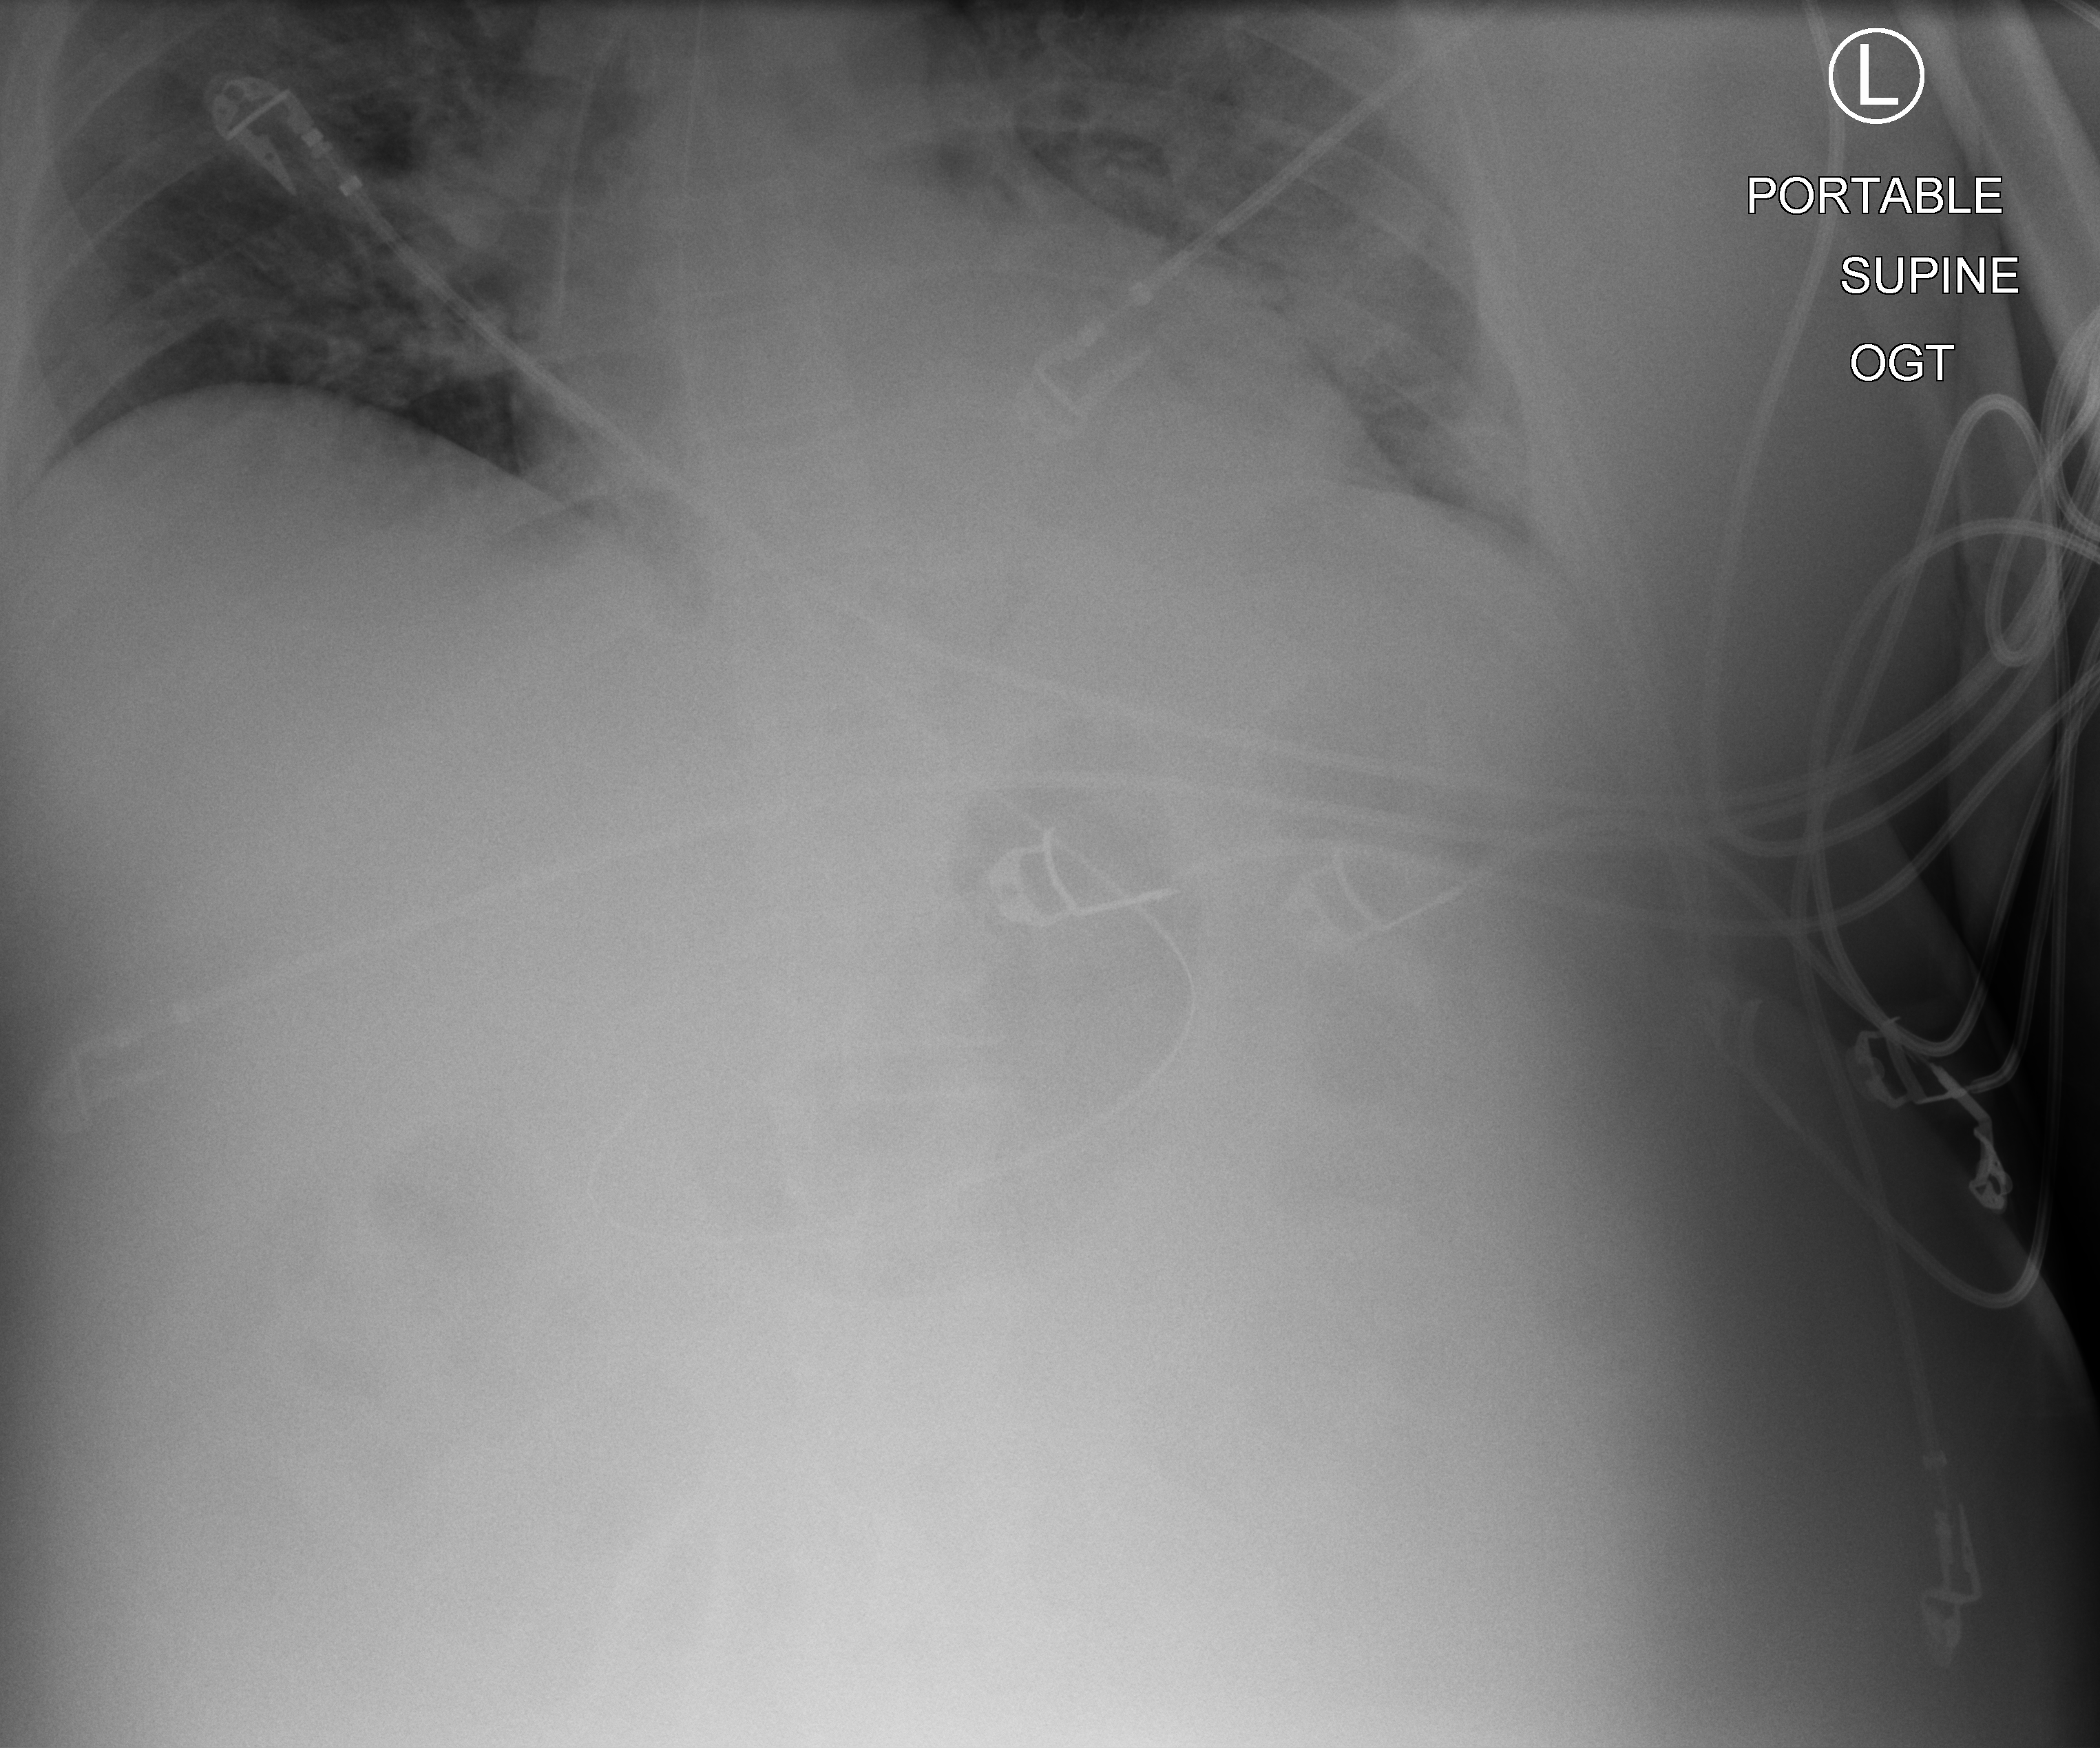
Abdomen X-ray (portable); anteroposterior (AP) projection. Adult patient hospitalised with COVID-19, age 18–59 years.
Admission-level facts for this patient (not findings on this image; timing relative to this image not recorded): diabetes (admission record): no; length of hospital stay: 16 days; mechanically ventilated during this hospital stay: yes.